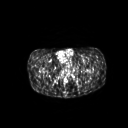
FDG PET of an extremity soft-tissue mass (from a PET/CT study), one axial slice; position 45 of 267 along the scan axis; 3.27 mm slice thickness; 128 × 128 image matrix. Male patient, age 59 years. From the clinical record (not read from this slice): histological type: pleiomorphic liposarcoma; grade: high; site of the primary tumour: left thigh.
Structures marked on this image (expert contour drawn on MRI and transferred to this co-registered scan by the dataset authors):
- gross tumour volume including surrounding oedema: bounding box [x1, y1, x2, y2] px = [70, 66, 78, 76]